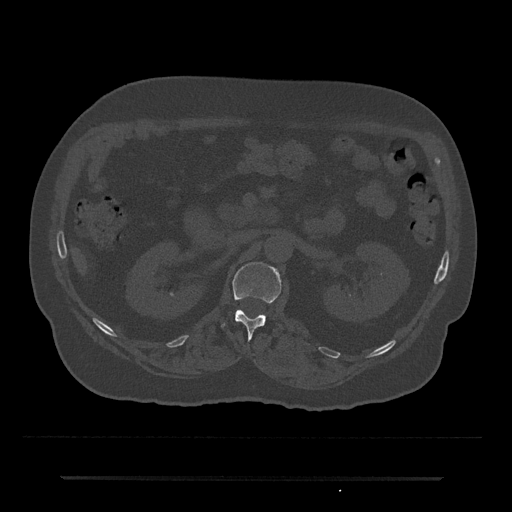
CT including the spine, one axial slice. Slice 65 of 797 in the series (ordered by position). Reconstruction kernel Br40s/3. Bone window (W 1800 / L 400 HU). 512 × 512 image matrix. Patient: male, 69 years. Case-level facts recorded for this patient, not image findings: primary cancer: prostate.
Outlined on this slice (semi-automatic segmentation, software-assisted and operator-edited):
- L1 vertebra: bounding box (x1, y1, x2, y2) in pixels: (222, 262, 282, 339)